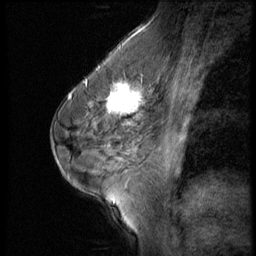
Breast MRI (dynamic contrast-enhanced), one sagittal slice. Slice 34 of 56 in the series (ordered by position). 3 images stored at this slice position (order not interpretable as contrast timing). 1.5 T. TE 4.2 ms, TR 9 ms. 256 × 256 image matrix, field of view 180 × 180 mm. Patient: female, 45 years. From the clinical record (not read from this slice): setting: breast cancer imaged before/during neoadjuvant chemotherapy; receptor status: HR-positive, HER2-negative.
Annotated regions visible in this slice (semi-automatically segmented with operator editing):
- analysis volume of interest (the breast-tissue region the enhancement analysis was run in; not a lesion): bounding box [x1, y1, x2, y2] px = [102, 77, 166, 129]
- tumour enhancement mask (voxels above the 140 % enhancement threshold inside the analysis volume of interest): [106, 79, 148, 128]